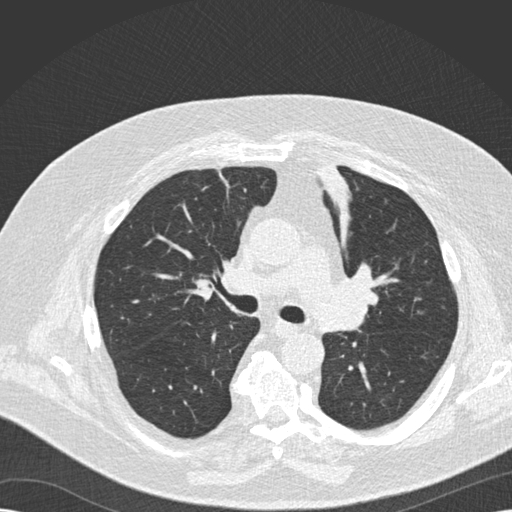
Low-dose screening chest CT, one axial slice. Position 105 of 173 along the scan axis. Reconstruction kernel B30f. 120 kVp. Lung window (W 1500 / L -600 HU). 512 × 512 image matrix.
Annotated regions visible in this slice (manually delineated by an expert):
- lesion 1 (tumor, upper lobe of left lung): bounding box (x1, y1, x2, y2) in pixels: (321, 166, 350, 204)